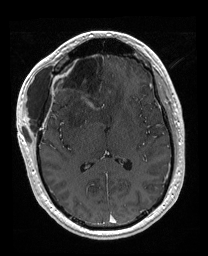
Brain MRI from a brain-tumour surgery series, one axial slice. Position 91 of 176 along the scan axis. T1-weighted post-contrast. 1 mm slice thickness. 208 × 256 image matrix, field of view 208 × 256 mm. From the clinical record (not read from this slice): histopathology: Astrocytoma; WHO grade: 4; IDH mutation: yes; tumour location: Right Orbitofrontal Anterior Temporal Insular.
Structures marked on this image (manually delineated by an expert):
- previous resection cavity: bounding box (x1, y1, x2, y2) in pixels: (56, 52, 106, 111)